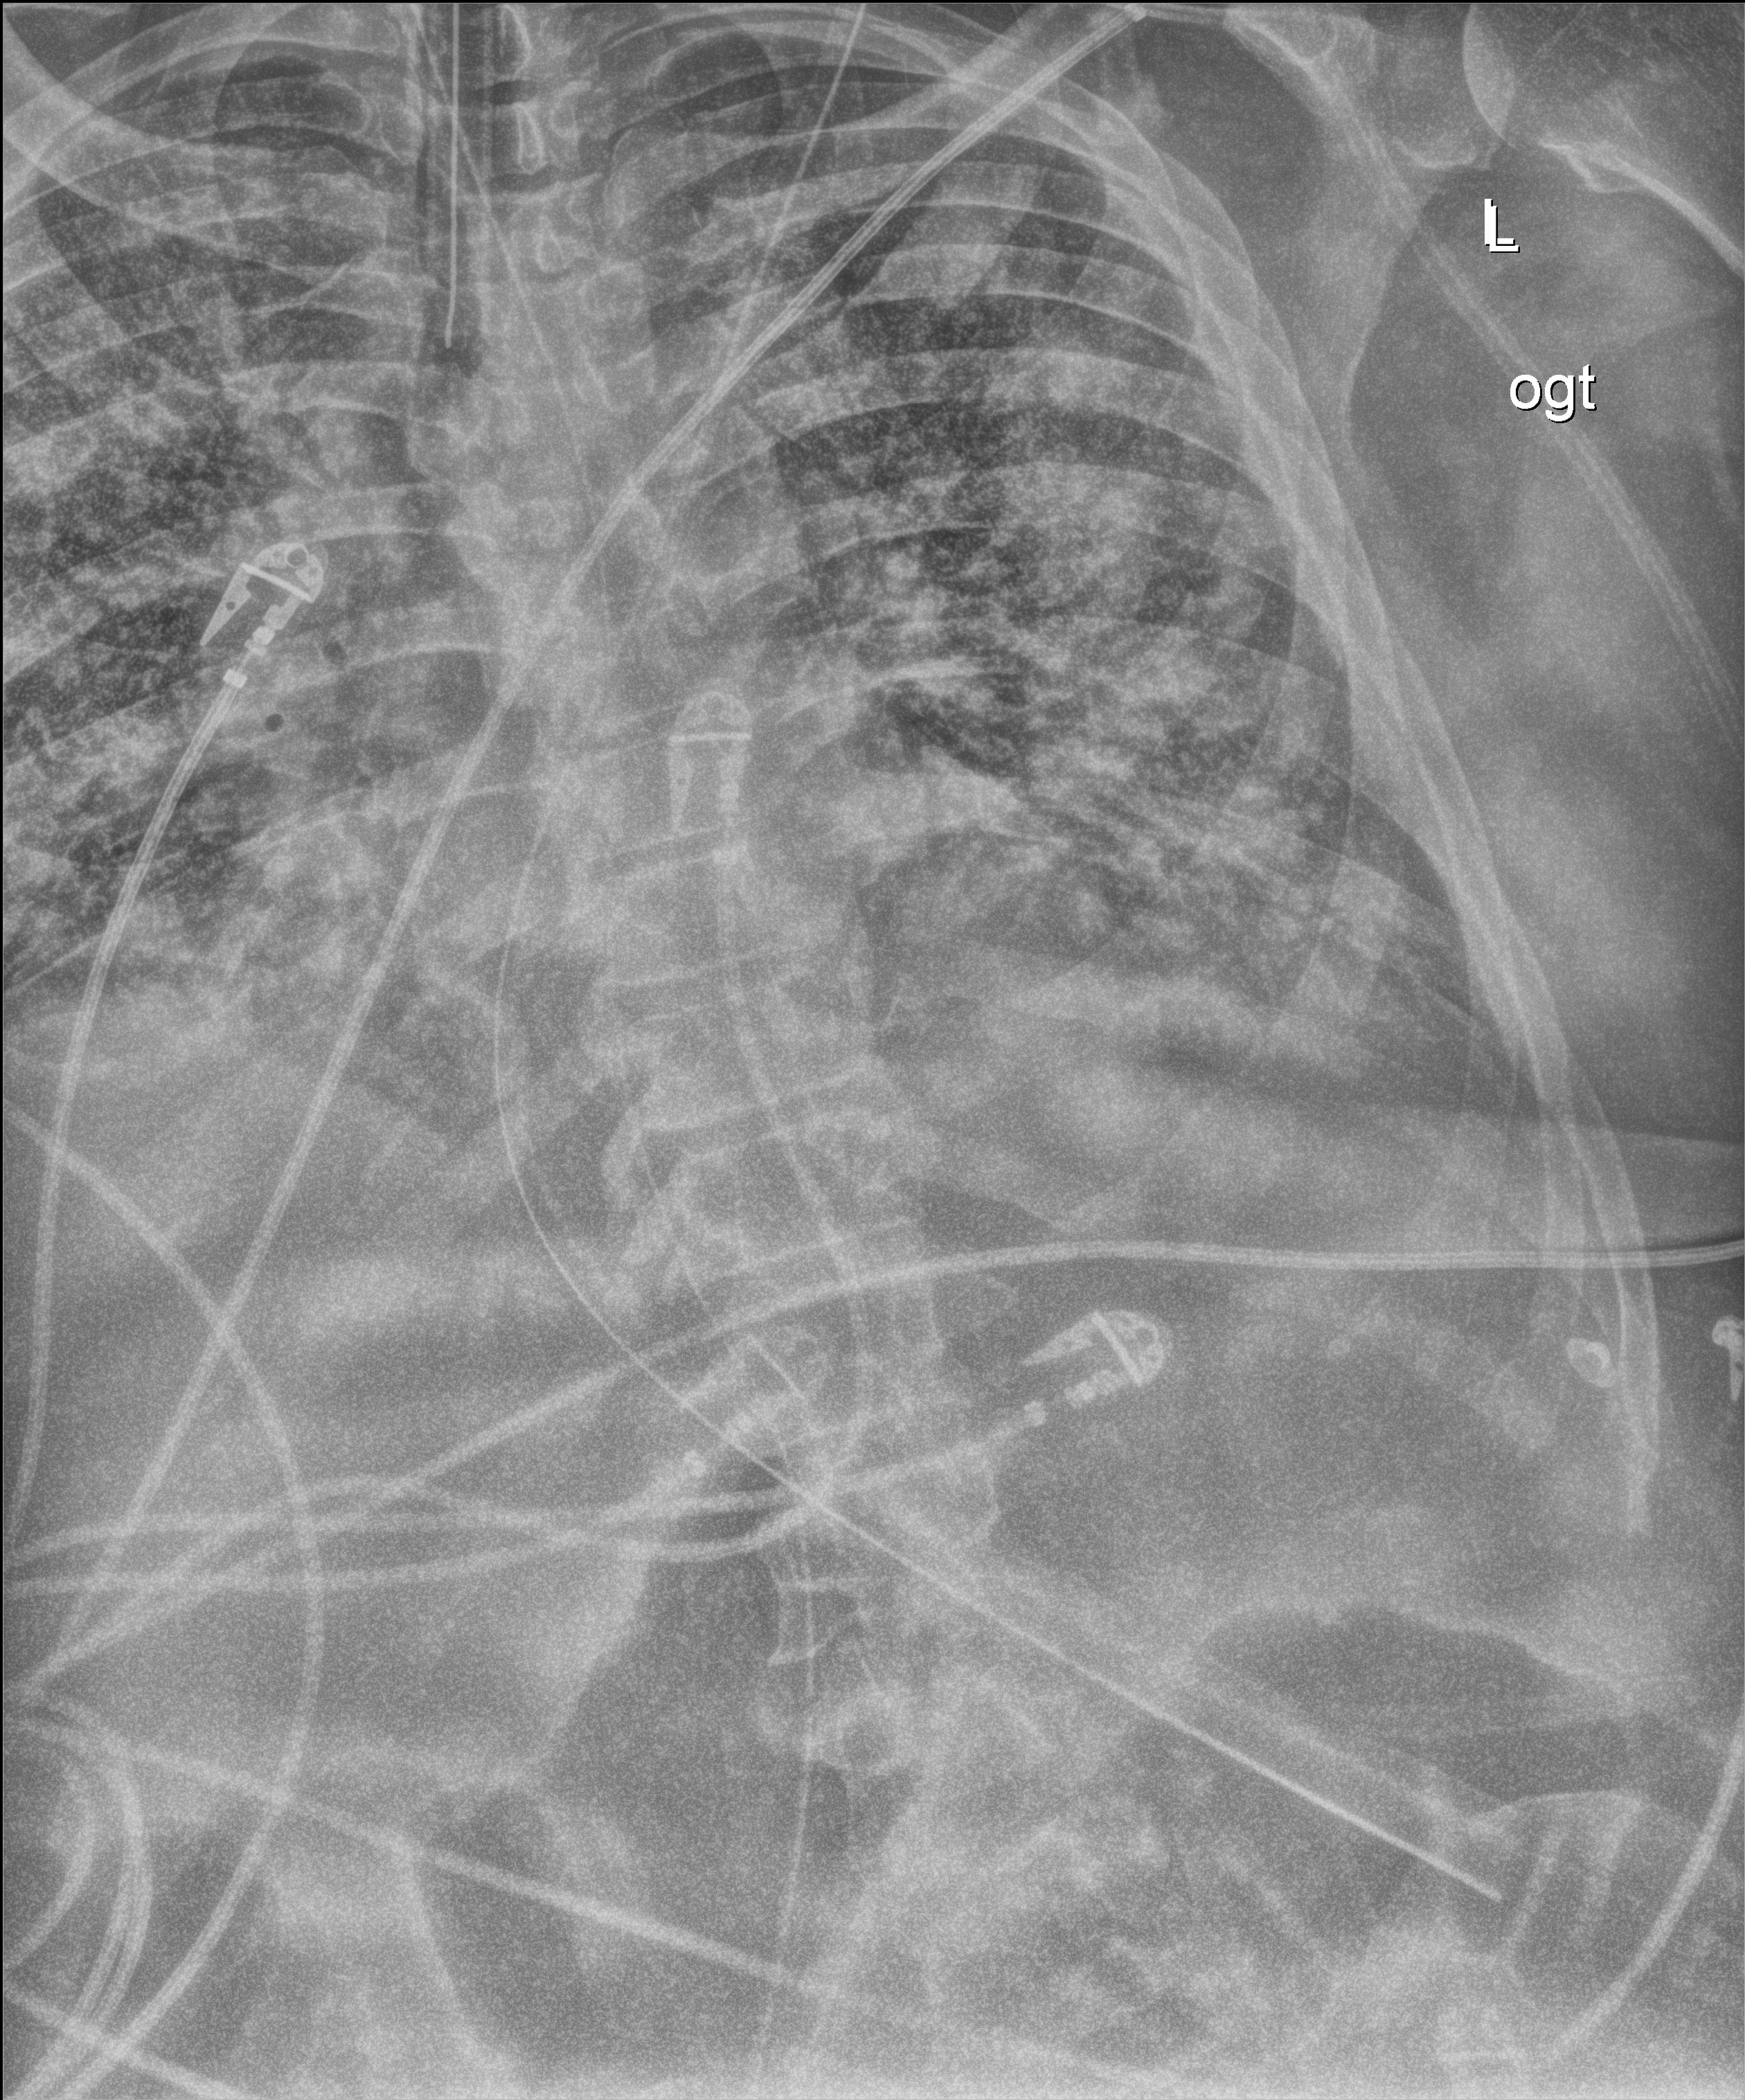
Portable chest radiograph; anteroposterior (AP) projection. Patient hospitalised with COVID-19; male, aged 60–74 years.
Admission-level facts for this patient (not findings on this image; timing relative to this image not recorded): diabetes (admission record): yes.